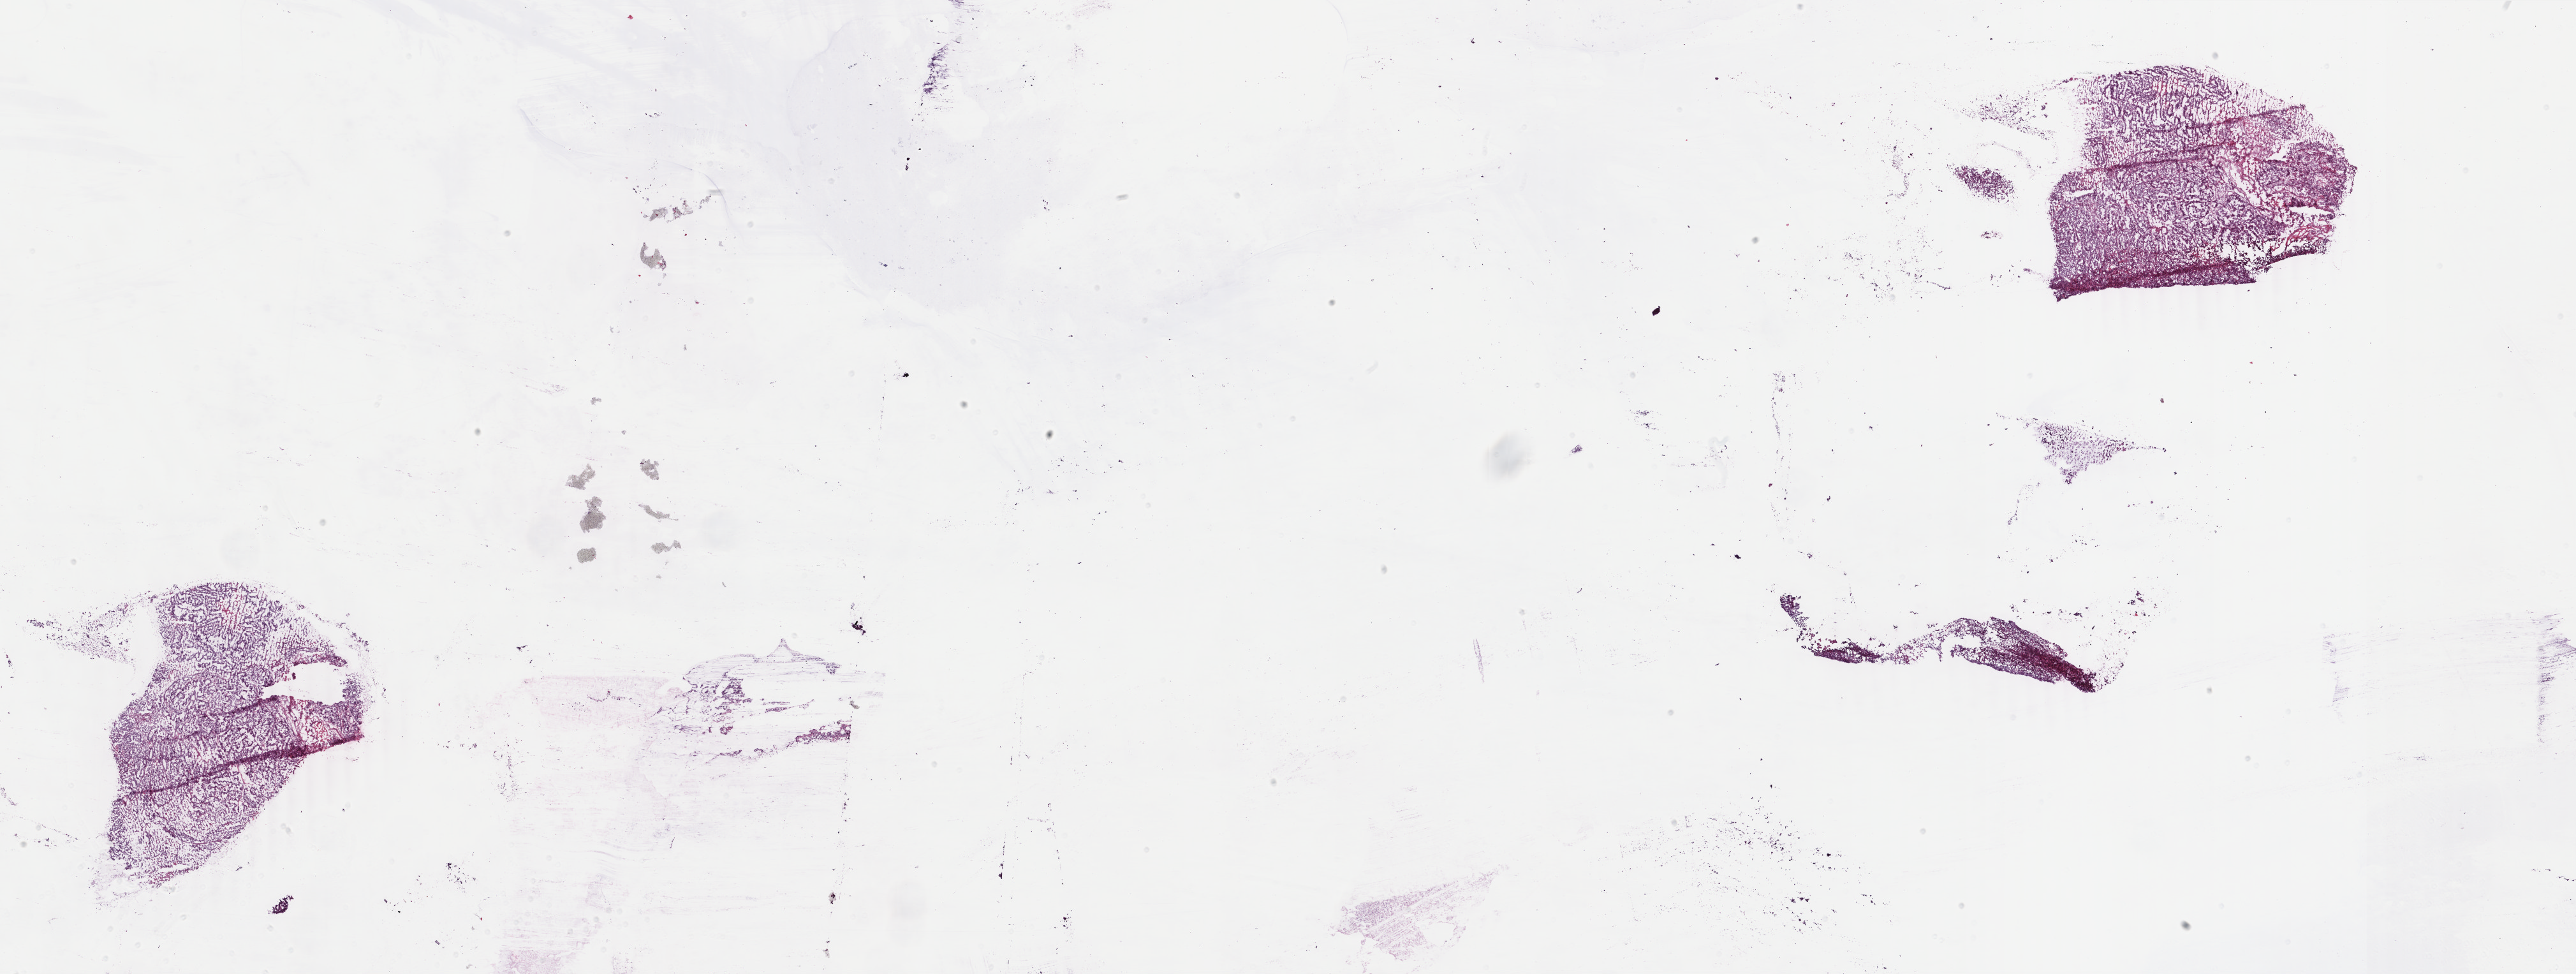
H&E whole-slide image, whole scanned area (about 32.1 x 12.1 mm) shown as a low-resolution overview, frozen section from the top of the tissue portion, uterus, primary tumour sample. Patient: female, age at initial diagnosis 47 years. Histologic grade: G2 (moderately differentiated). Composition of this section per pathologist review: tumour cells 85%, tumour nuclei 90%, normal cells 0%, stromal cells 5%, necrosis 10%. Inflammatory infiltration, as recorded: lymphocyte infiltration 0%, monocyte infiltration 0%, neutrophil infiltration 0%.
* FIGO stage: IB
* diagnosis: Endometrioid adenocarcinoma, NOS
* lymph nodes positive (case pathology): 0 of 3 examined